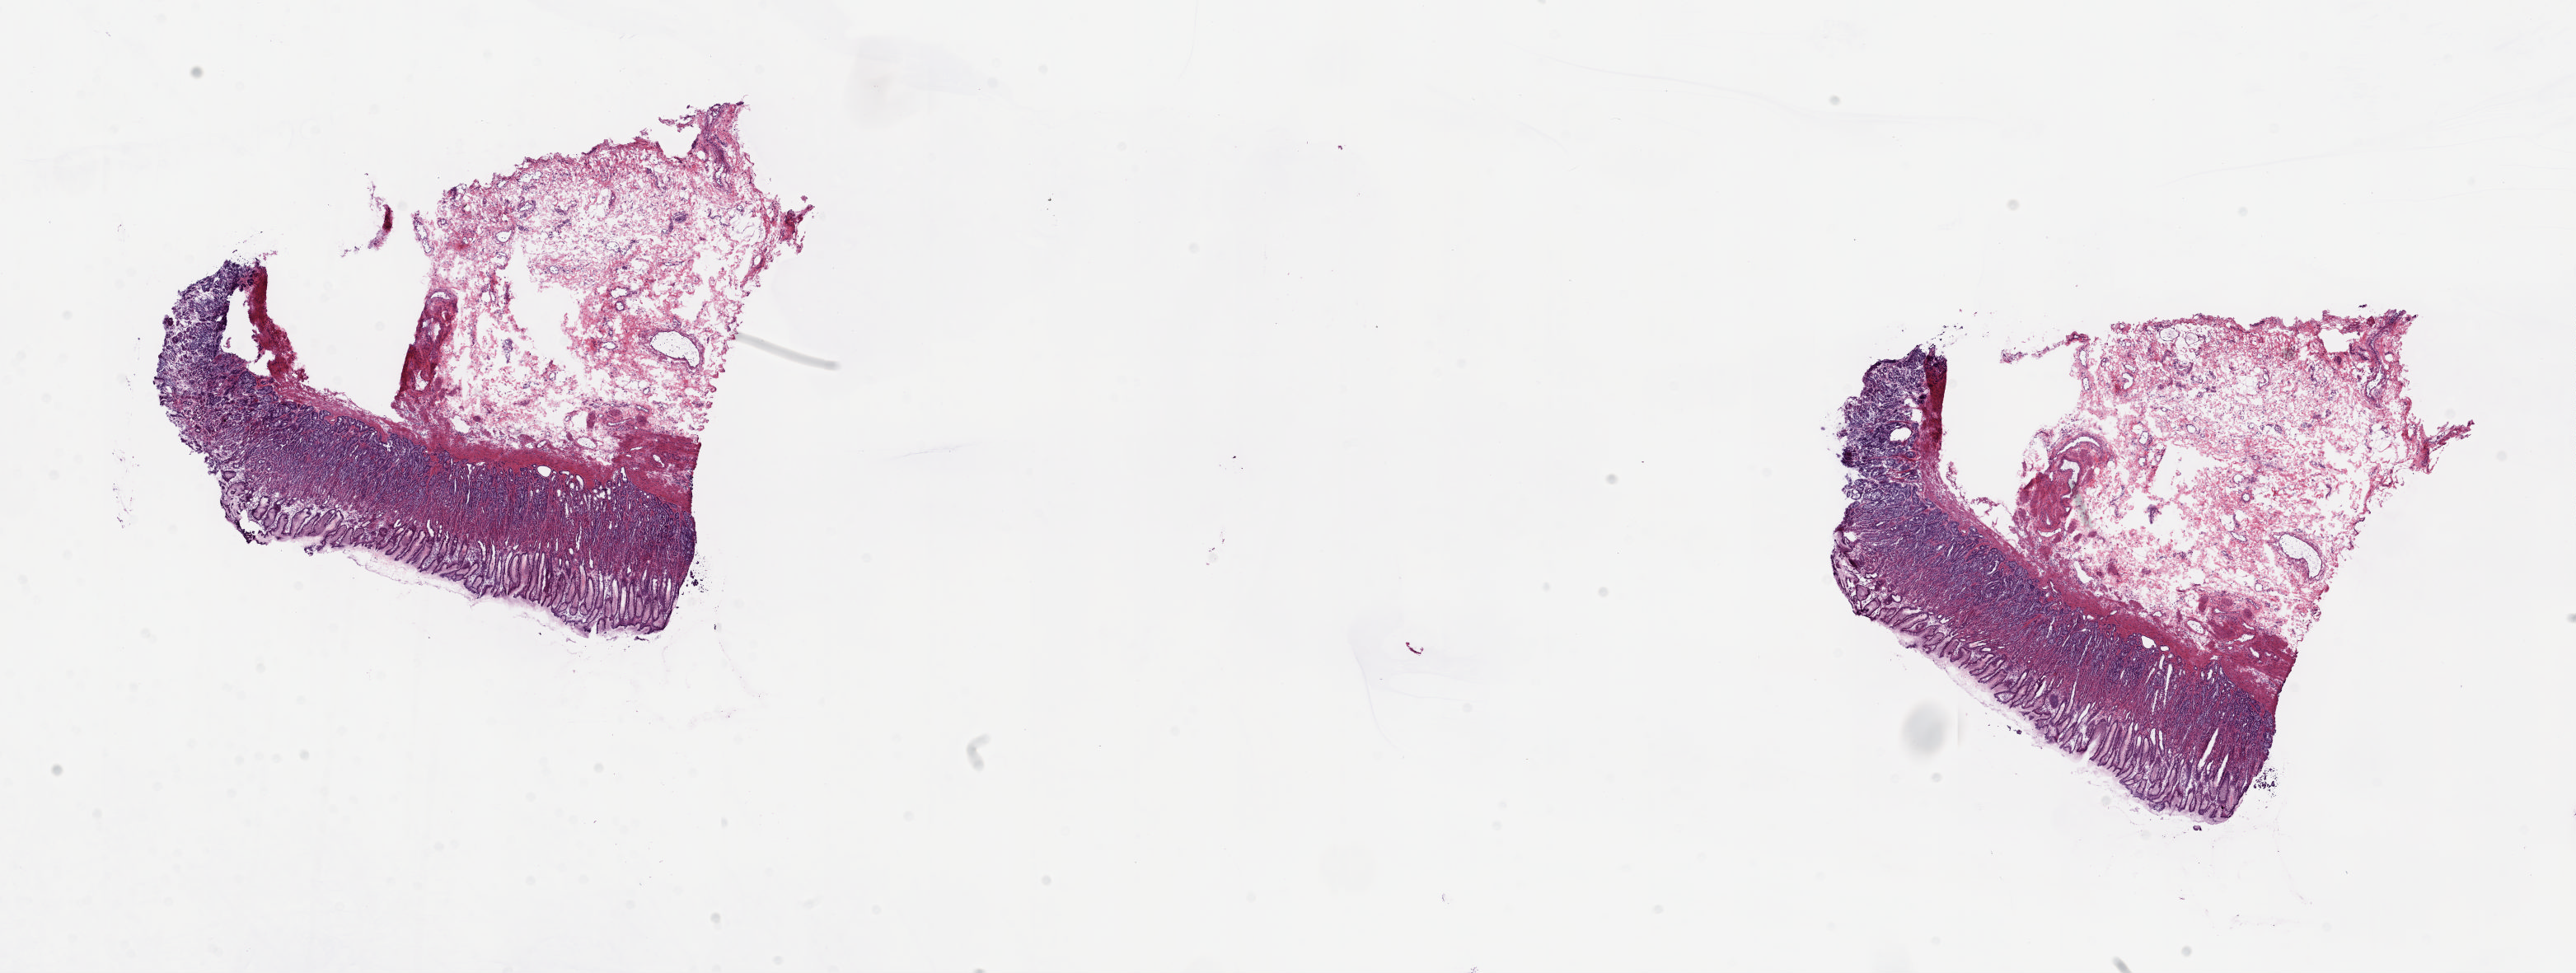
Digitized H&E tissue section (whole slide), low-resolution overview of the scanned area, about 24.8 x 9.4 mm (acquisition: 20x scan). Frozen section. Solid tissue normal (non-tumour tissue) sample from the esophagus. Patient: female, age at initial diagnosis 84 years. Pathologist review of this section (percent, as recorded): tumour cells 0%, tumour nuclei 0%, normal cells 100%, stromal cells 0%, necrosis 0%. Inflammatory infiltration, as recorded: lymphocyte infiltration 0%, monocyte infiltration 0%, neutrophil infiltration 0%.
• this section: solid tissue normal (non-tumour) sample from the same patient
• patient diagnosis: Adenocarcinoma, NOS (lower third of esophagus)